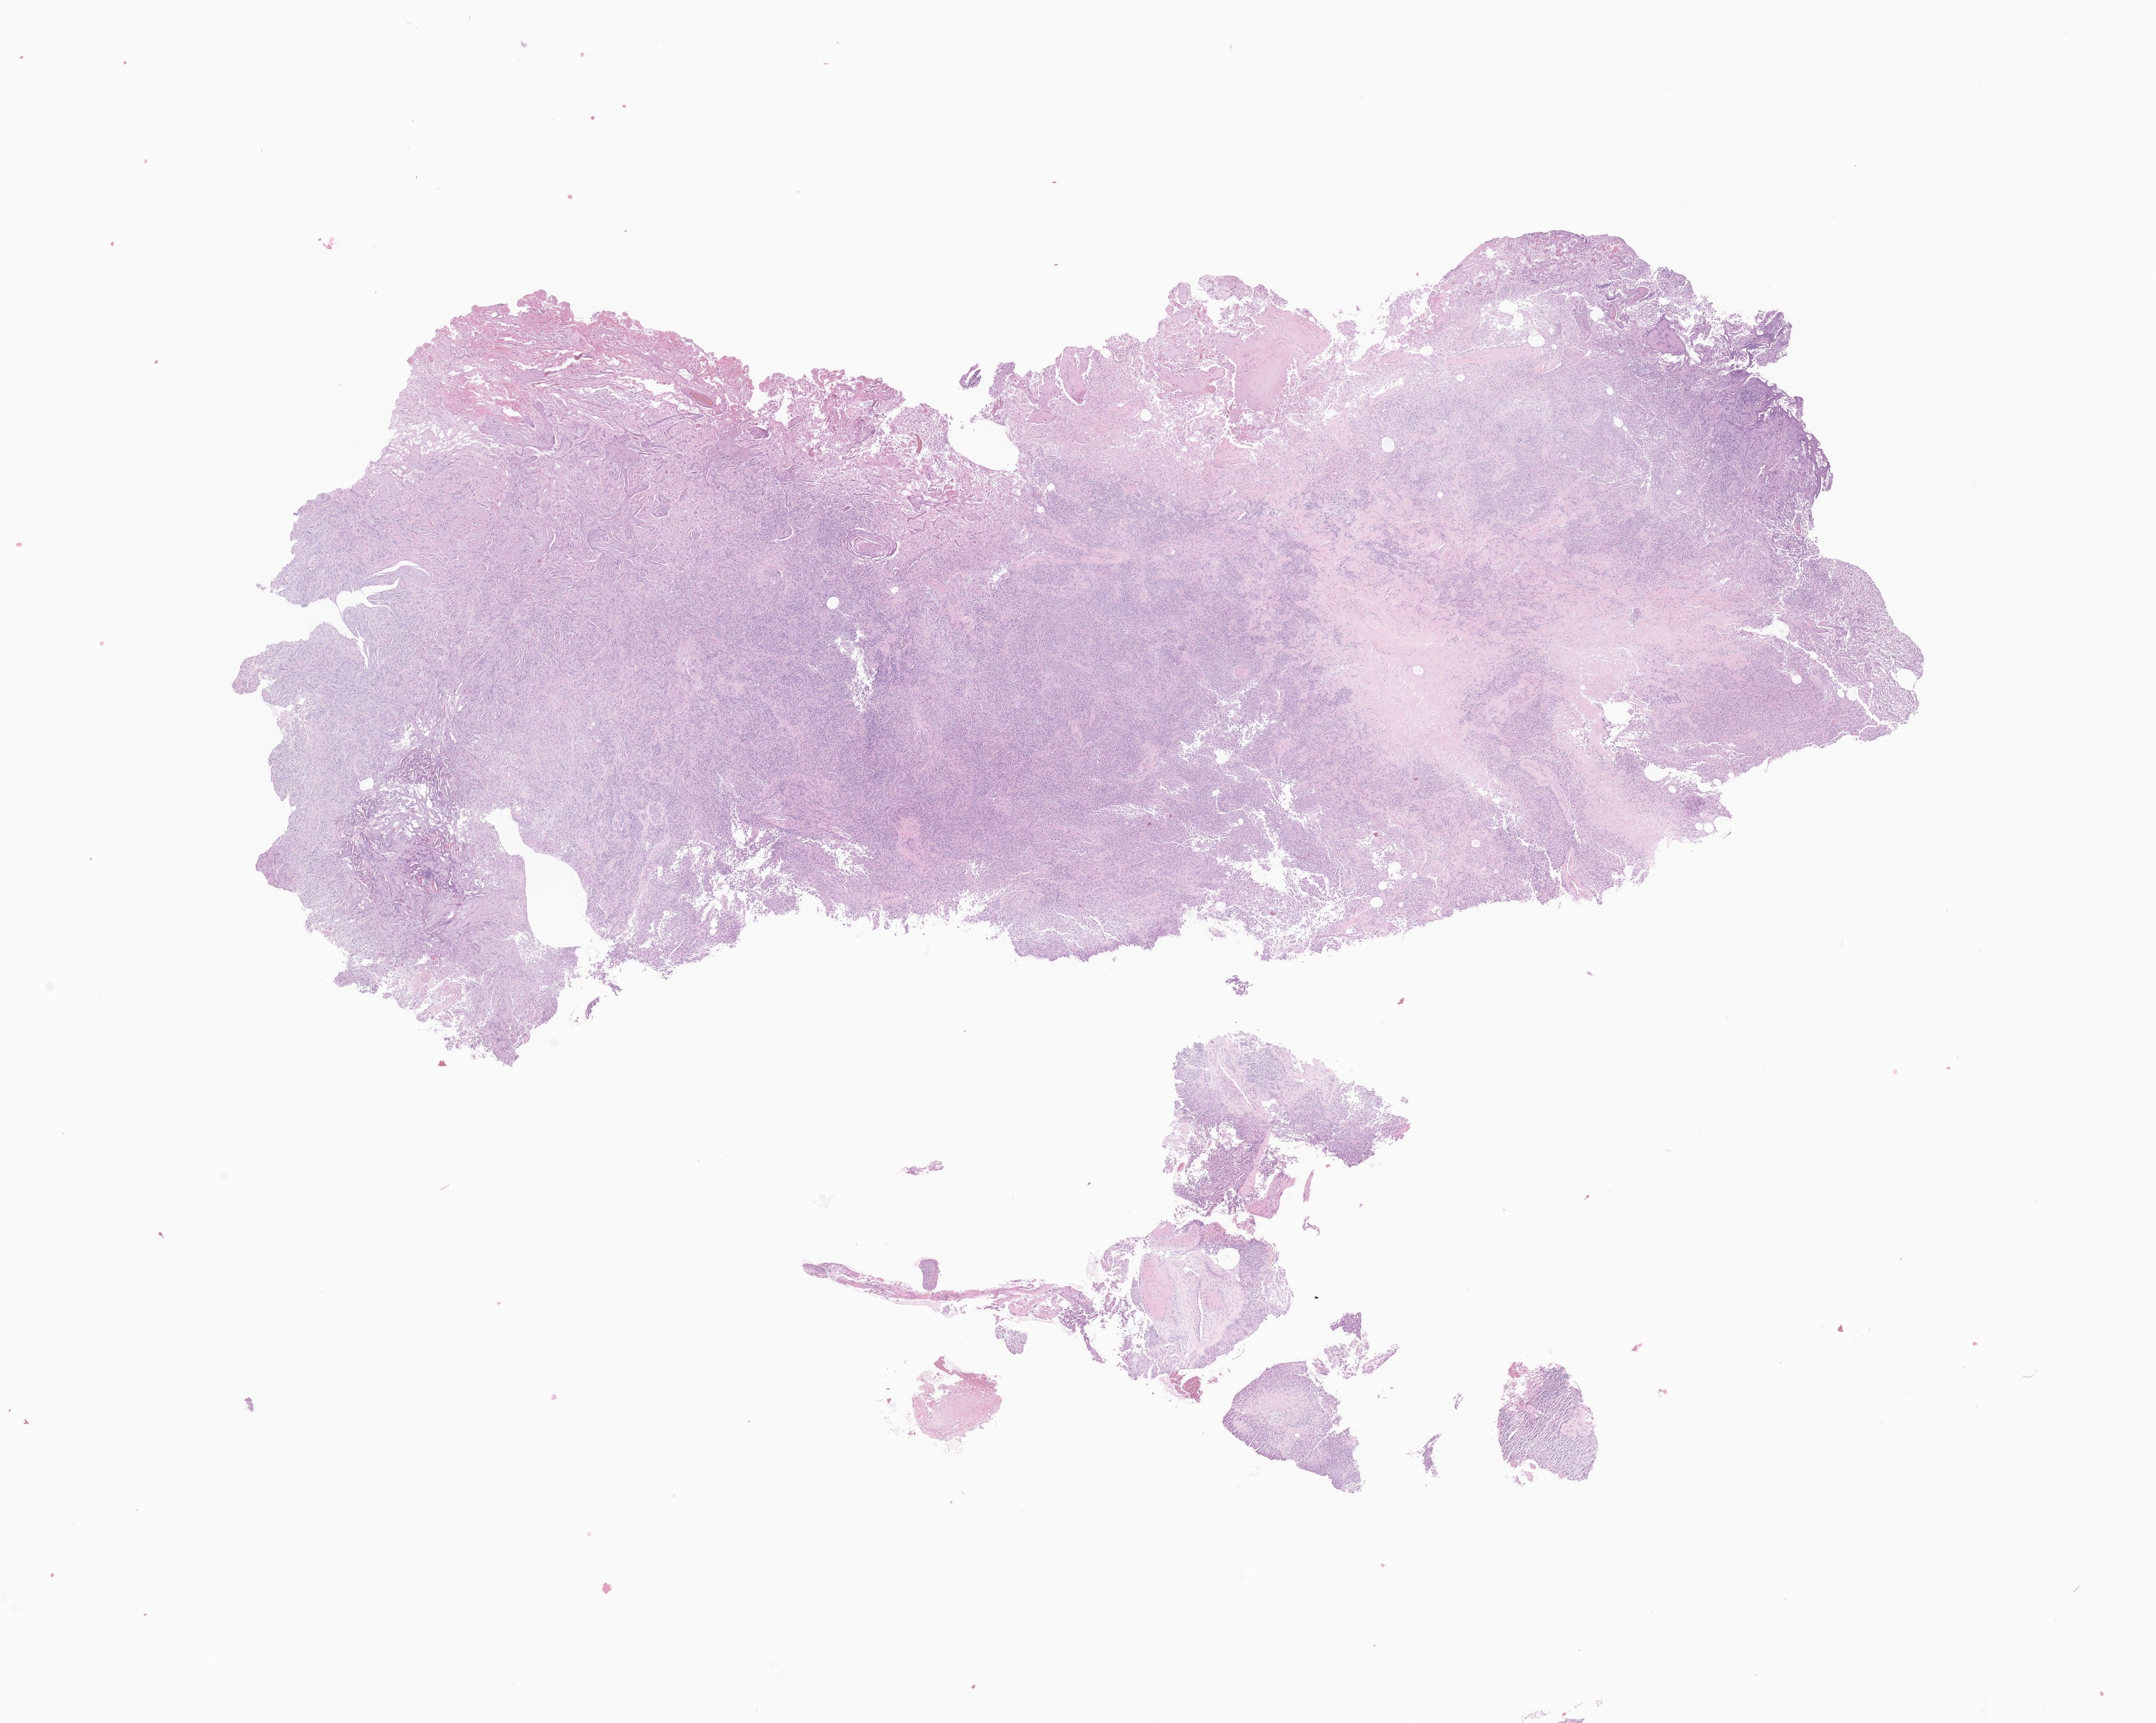
Digitized haematoxylin and eosin-stained section of tumor tissue from the temporal lobe, low-resolution overview of the scanned area, about 17.3 x 13.8 mm; formalin-fixed, paraffin-embedded (FFPE) tissue. Male patient, age 50 months (4 years 2 months).
- recorded diagnosis: Glioma, malignant